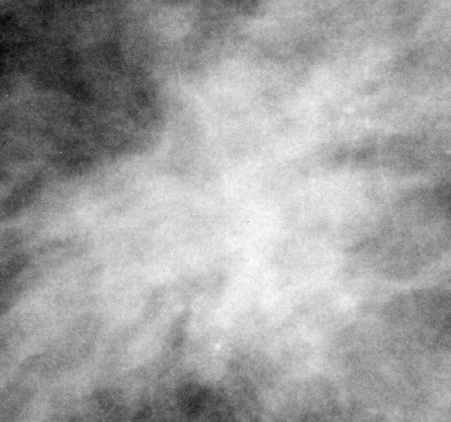
Crop from a digitized film mammogram around one marked abnormality; right breast; CC view.
Mass, shape irregular, margins spiculated; BI-RADS assessment category 5; pathology (as recorded): malignant.